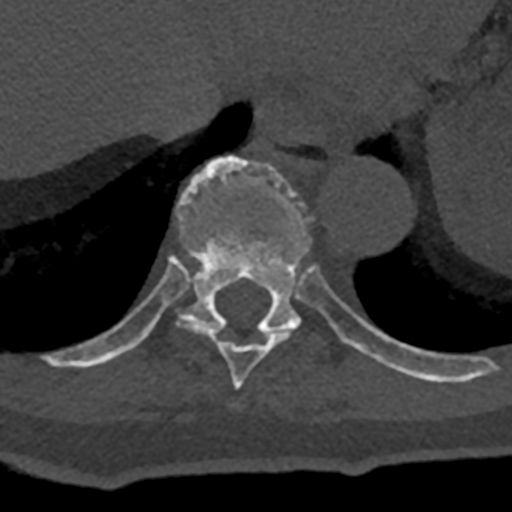
CT including the spine, one axial slice. Slice 626 of 797 in the series (ordered by position). Reconstruction kernel Br40s/3. Bone window (W 1800 / L 400 HU). 0.5 mm slice thickness. 512 × 512 image matrix, field of view 160 × 160 mm. Male patient, age 74 years. From the clinical record (not read from this slice): primary cancer: renal; vertebrae with lytic lesions (as recorded): T10, L1, L2, L3, L4, L5.
Structures marked on this image (semi-automatically segmented with operator editing):
- T10 vertebra: box from (x=70, y=156) to (x=432, y=382) px
- T9 vertebra: (x=178, y=318)–(x=294, y=390)